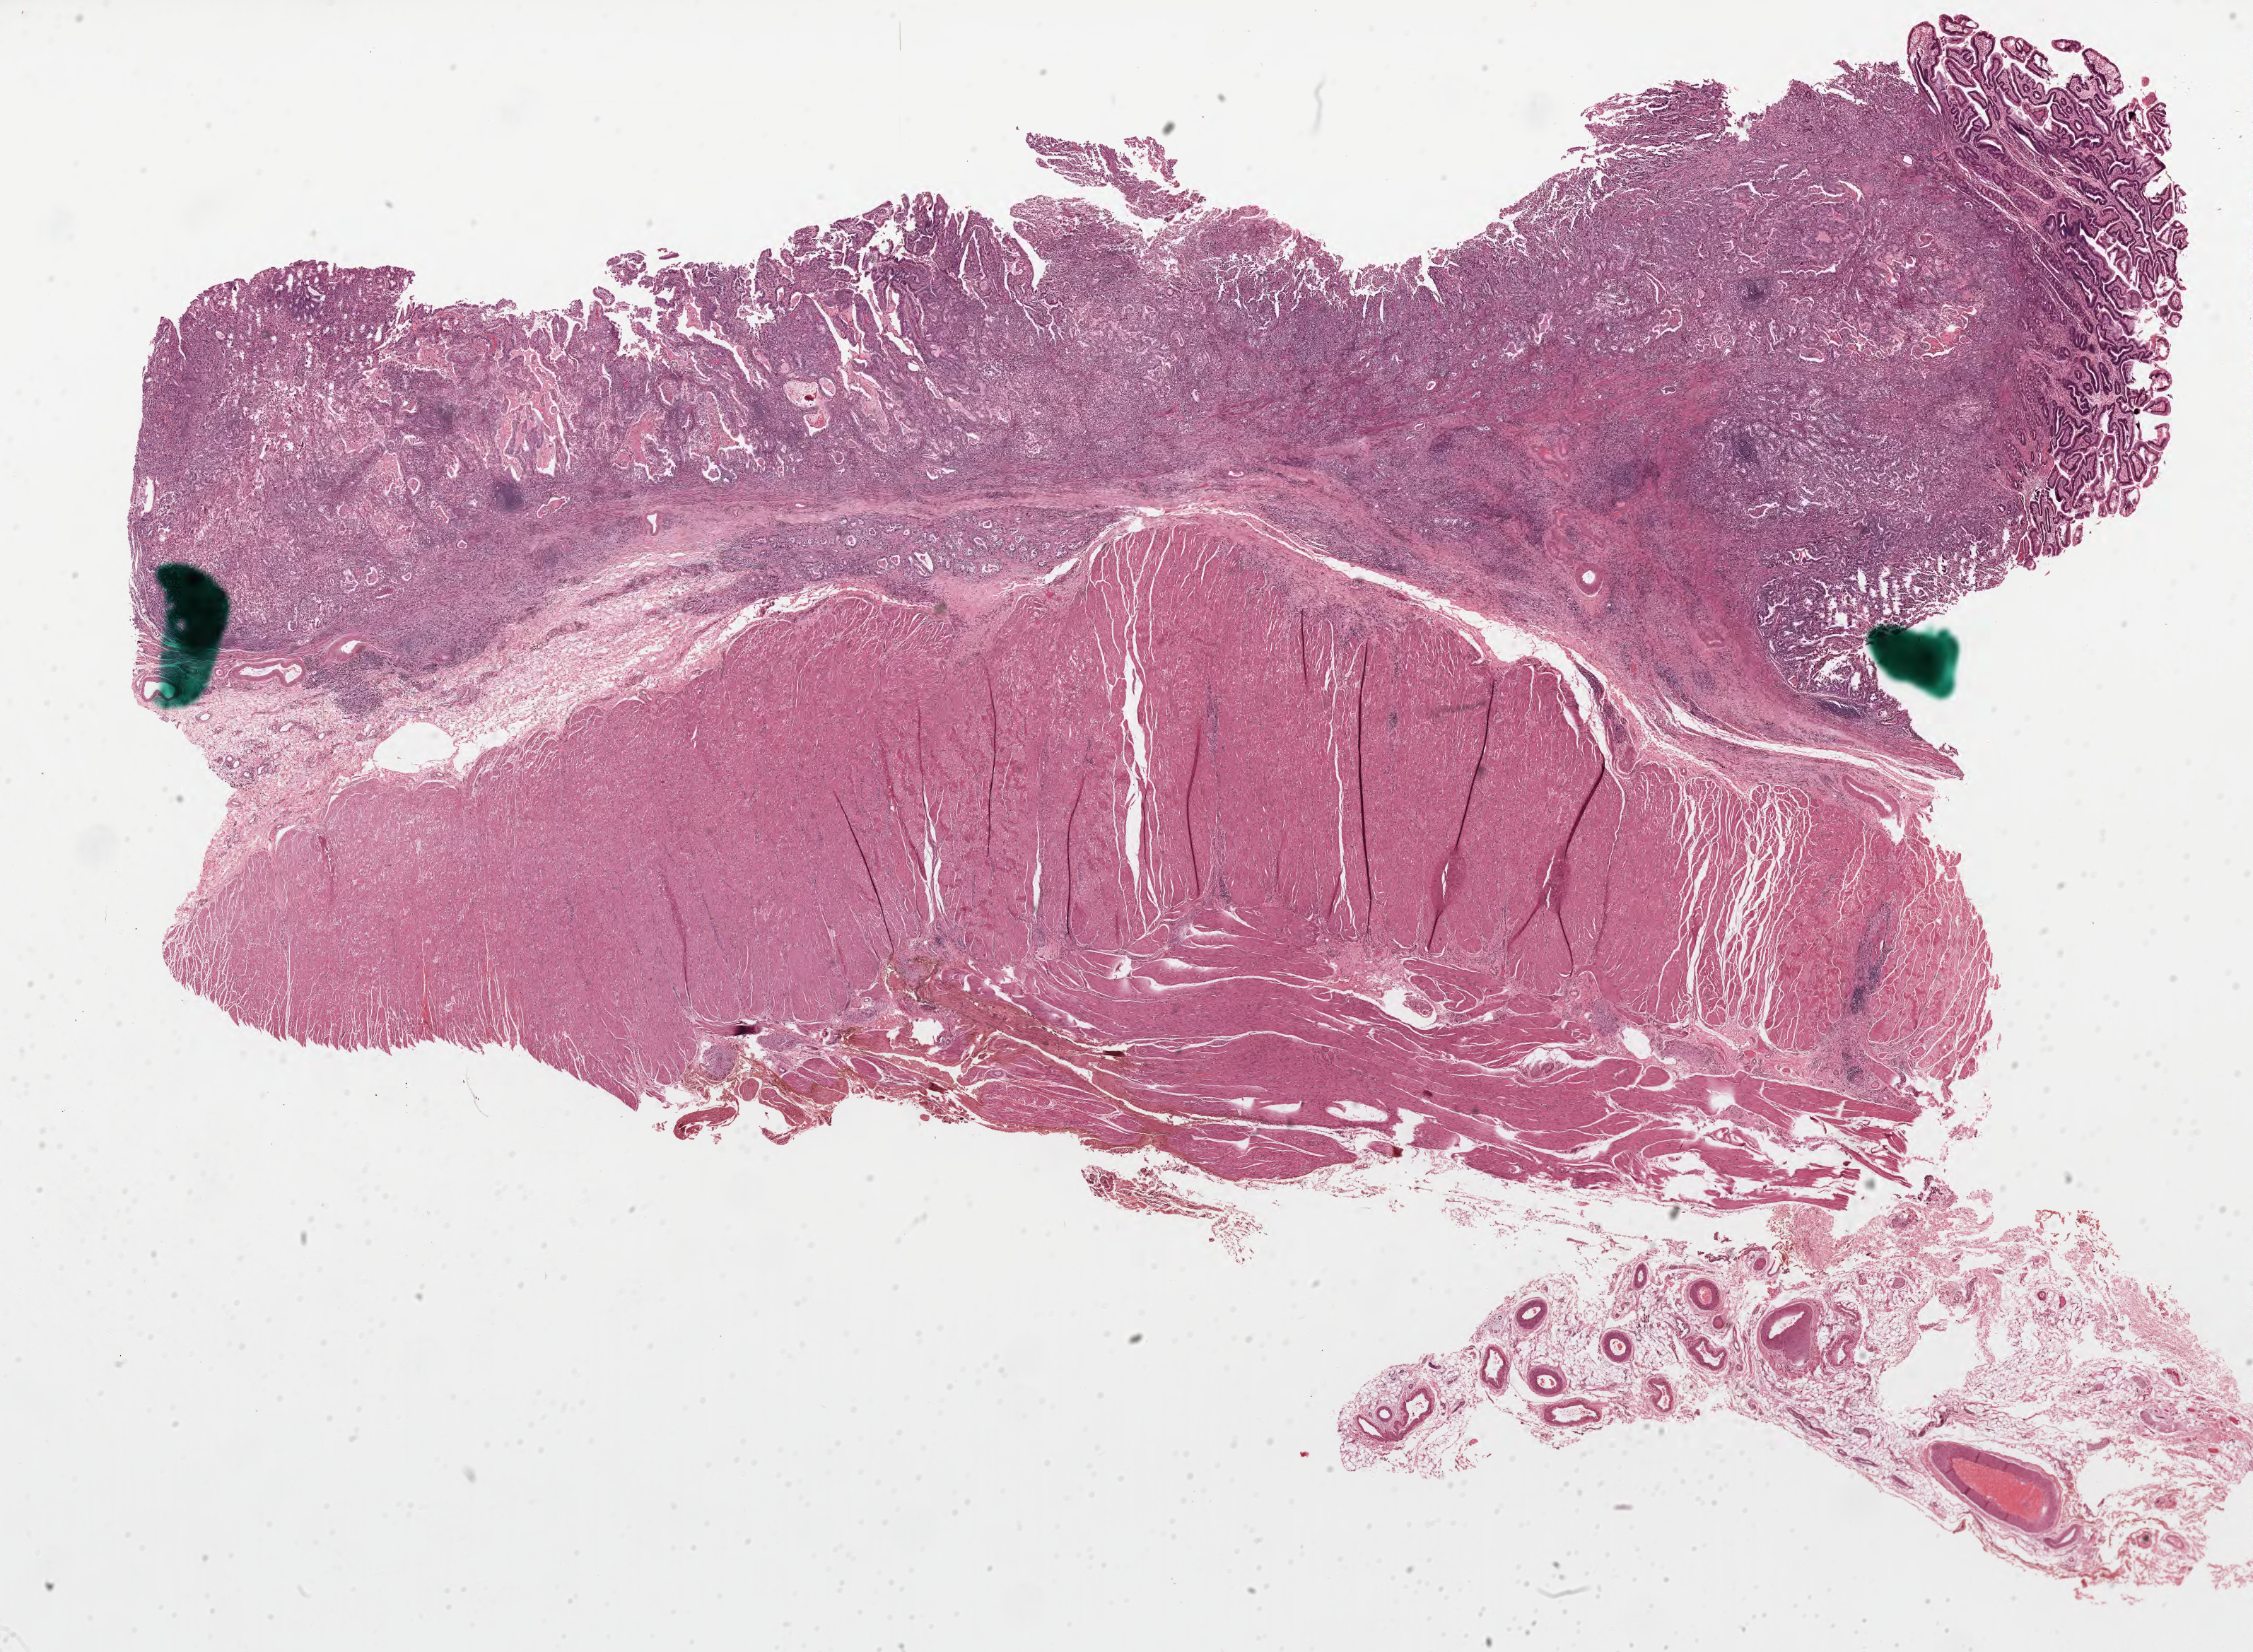
Digitized H&E-stained tissue section (whole slide), shown as a low-resolution overview of the whole scanned area (about 25.7 x 18.8 mm). Formalin-fixed paraffin-embedded (FFPE) diagnostic section. Esophagus, primary tumour sample. Male patient; age at initial diagnosis 51 years. Histologic grade: G3 (poorly differentiated).
Lymph nodes positive (case pathology): 14 of 39 examined. AJCC pathologic stage: IIIC (7th edition). Histologic diagnosis: Adenocarcinoma, NOS (lower third of esophagus).